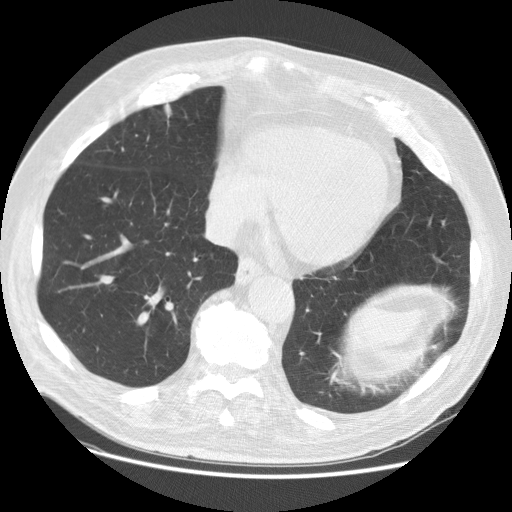
Low-dose screening chest CT, axial slice, baseline screening round, lung window (W 1500 / L -600 HU), slice 93 of 129 in the series, 512 × 512 image matrix. Male participant, aged 74 years at enrolment. Former smoker at enrolment.
Lesion marked by an expert reader, bounding box <148,92,187,139> (left, top, right, bottom; pixels). Screening reader's record for this exam (one nodule recorded; not confirmed to be the boxed lesion): non-calcified nodule or mass ≥4 mm, right middle lobe, 24 × 24 mm, spiculated (stellate) margins, soft tissue attenuation. Official screen result: positive, change unspecified: nodule(s) >= 4 mm or enlarging nodule(s), mass(es), or other non-specific abnormalities suspicious for lung cancer. Participant outcome: lung cancer diagnosed 296 days after this screen — papillary adenocarcinoma, NOS, right middle lobe, well differentiated (G1), stage IA (AJCC 6th edition), 20 mm at pathology.